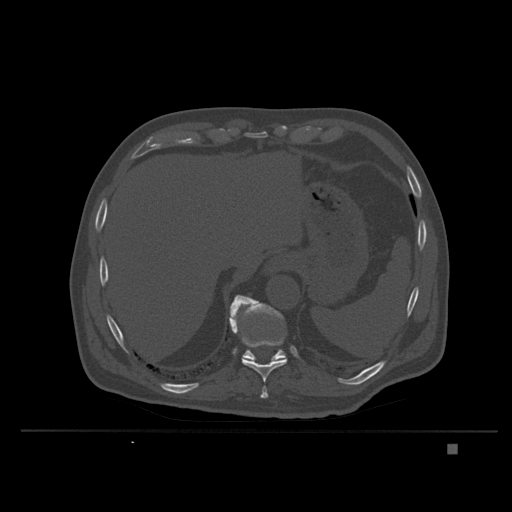
CT including the spine, one axial slice. Position 190 of 435 along the scan axis. Bone window (W 1800 / L 400 HU). 1.5 mm slice thickness. 512 × 512 image matrix, field of view 434 × 434 mm. Male patient, age 73 years. Case-level facts recorded for this patient, not image findings: primary cancer: skin.
Outlined on this slice (semi-automatically segmented with operator editing):
- T10 vertebra: bounding box (x1, y1, x2, y2) in pixels: (230, 321, 287, 383)
- T11 vertebra: (229, 295, 287, 363)
- T9 vertebra: (261, 386, 268, 399)